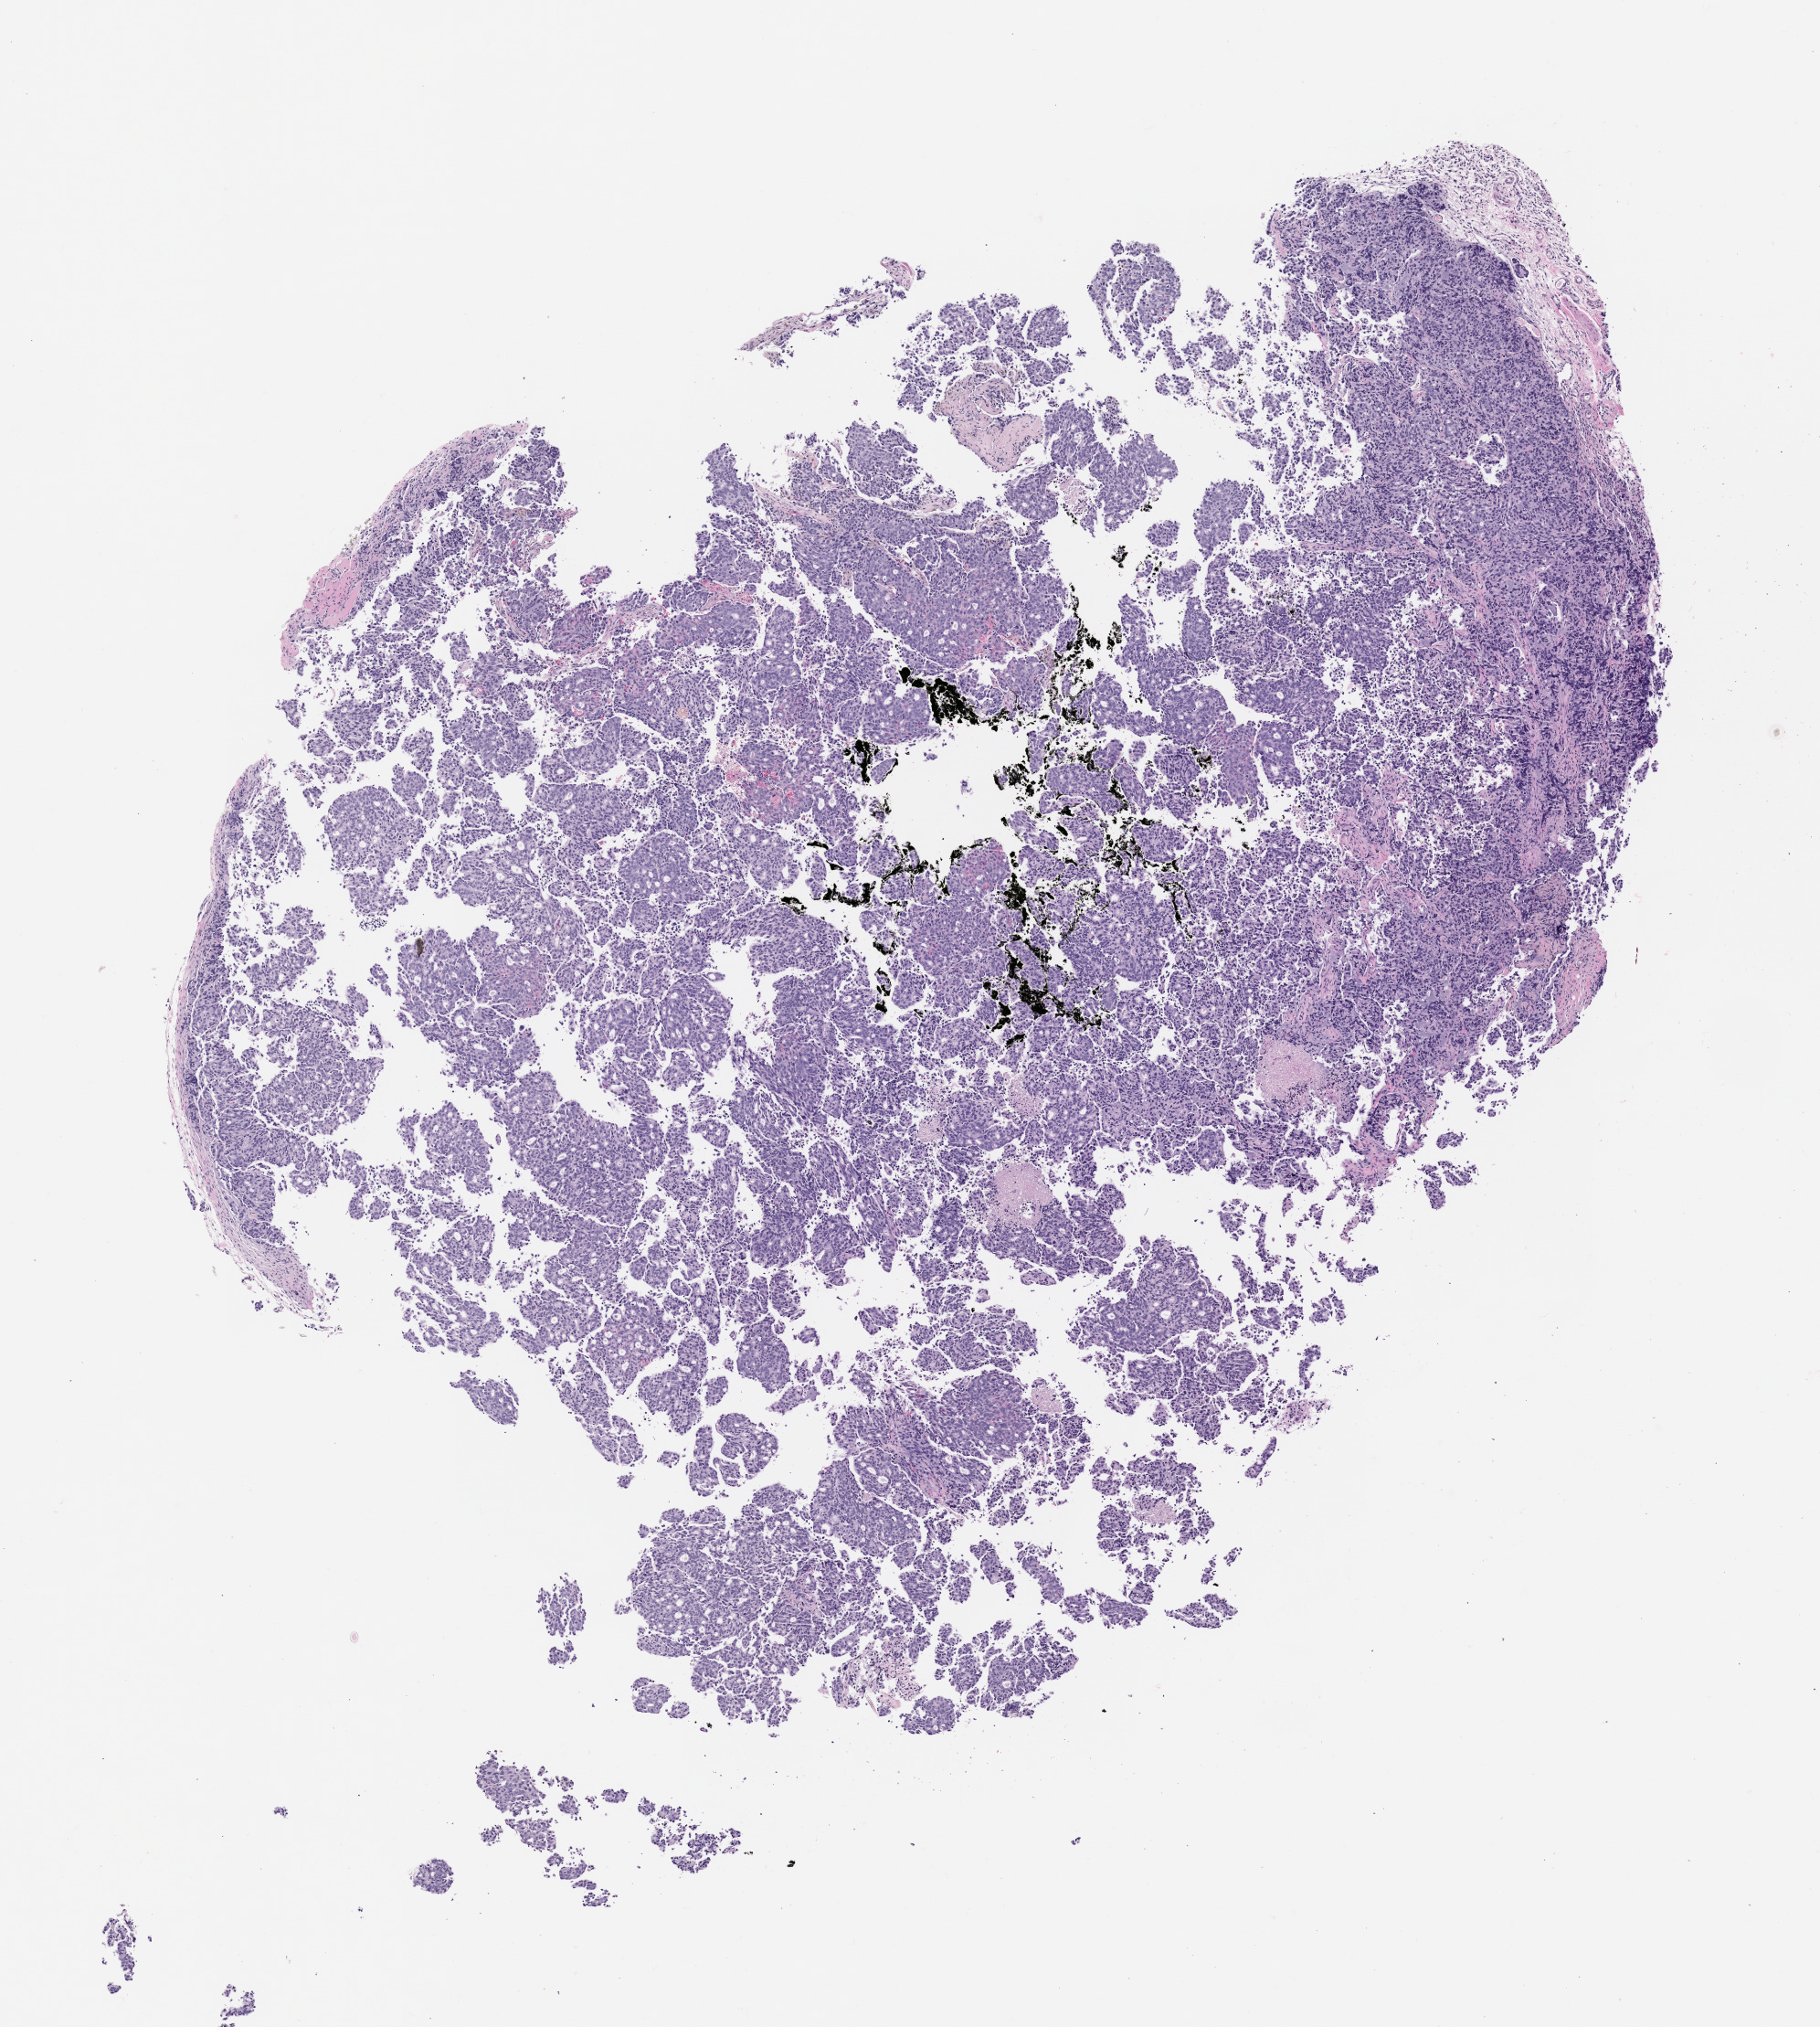
Whole-slide image, hematoxylin and eosin (H&E): patient-derived xenograft (human tumor grown in a mouse), low-resolution overview of the scanned area, about 8.0 x 8.9 mm; formalin-fixed, paraffin-embedded (FFPE) tissue; originating tumor site category: prostate.
Originating patient diagnosis: Prostate Carcinoma.